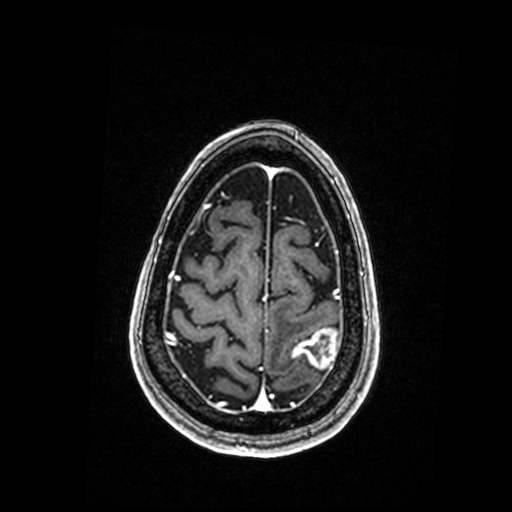
Brain MRI from a brain-tumour surgery series, one axial slice; T1-weighted post-contrast; 0.98 mm slice thickness; 512 × 512 image matrix, field of view 250 × 250 mm. Case-level facts recorded for this patient, not image findings: histopathology: Metastastic Carcinoma, Poorly Differentiated; tumour location: Left Parietal.
Outlined on this slice (expert manual segmentation):
- tumour: bounding box (x1, y1, x2, y2) in pixels: (293, 330, 337, 369)